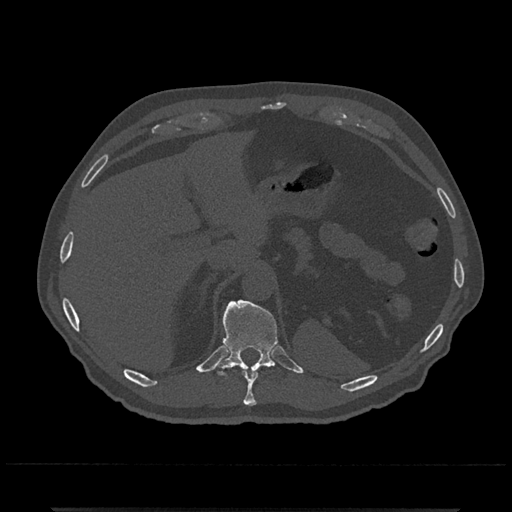
CT including the spine, one axial slice. Position 511 of 797 along the scan axis. Bone window (W 1800 / L 400 HU). 512 × 512 image matrix, field of view 393 × 393 mm. Male patient, age 67 years. Case-level facts recorded for this patient, not image findings: primary cancer: prostate.
Structures marked on this image (semi-automatically segmented with operator editing):
- T10 vertebra: bounding box <243,371,258,406> (left, top, right, bottom; pixels)
- T11 vertebra: <215,300,278,376>